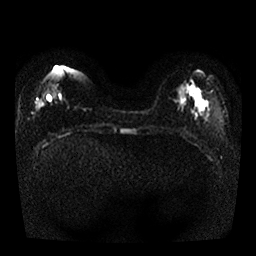
Breast MRI, one axial slice. Position 11 of 25 along the scan axis. Diffusion-weighted series; image 2 of 4 stored at this slice position (different b-values; order by instance number). 1.5 T. 4 mm slice thickness. 256 × 256 image matrix, field of view 330 × 330 mm. Female patient.
Outlined on this slice (expert manual segmentation):
- tumour on diffusion-weighted imaging: bounding box (x1, y1, x2, y2) in pixels: (193, 91, 199, 95)